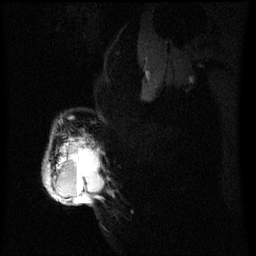
Breast MRI (dynamic contrast-enhanced), one sagittal slice. Dynamic contrast-enhanced series, image 2 of 3 at this slice position (ordered by acquisition). 1.5 T. TE 4.2 ms, TR 8 ms. 2.2 mm slice thickness. 256 × 256 image matrix, field of view 200 × 200 mm. Patient: female, 50 years.
Structures marked on this image (semi-automatically segmented with operator editing):
- analysis volume of interest (the breast-tissue region the enhancement analysis was run in; not a lesion): box from (x=45, y=134) to (x=105, y=205) px
- tumour enhancement mask (voxels above the 70 % enhancement threshold inside the analysis volume of interest): (x=45, y=140)–(x=97, y=205)